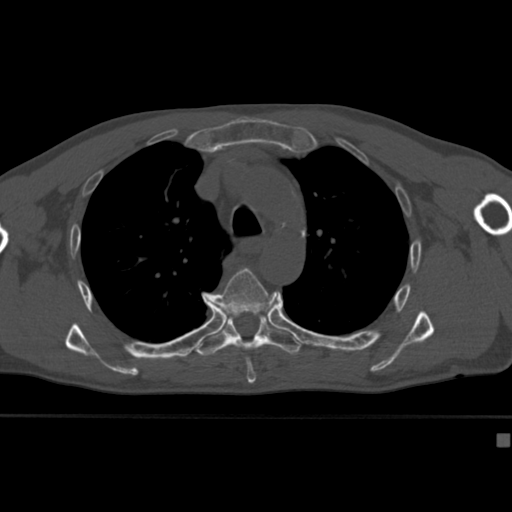
CT including the spine, one axial slice; 120 kVp; bone window (W 1800 / L 400 HU); 512 × 512 image matrix, field of view 337 × 337 mm. Male patient, age 64 years. From the clinical record (not read from this slice): primary cancer: uterus; vertebrae with lytic lesions (as recorded): T1, T4, T5, T7, L5.
Outlined on this slice (semi-automatic segmentation, software-assisted and operator-edited):
- T5 vertebra: bounding box [x1, y1, x2, y2] px = [207, 268, 278, 382]
- T6 vertebra: [196, 310, 302, 361]